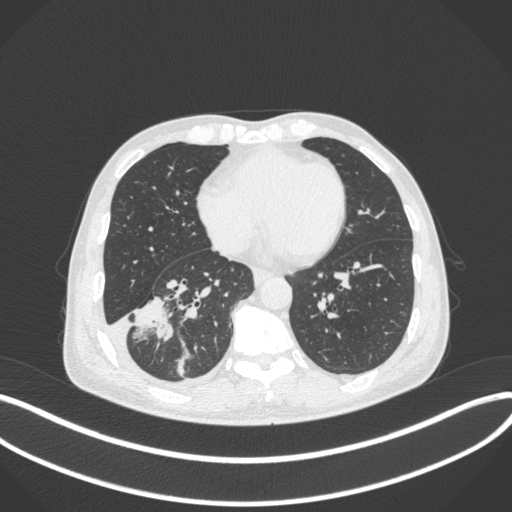
Chest CT, one axial slice; position 140 of 385 along the scan axis; 120 kVp; lung window (W 1500 / L -600 HU); 512 × 512 image matrix, field of view 400 × 400 mm. Patient: male, 64 years. Case-level facts recorded for this patient, not image findings: clinical TNM (as recorded): T3 N0 M0; histopathological grade: G2-3.
Structures marked on this image (rectangle marked by the reading radiologist):
- lung tumour (recorded histology: adenocarcinoma): bounding box <126,291,176,352> (left, top, right, bottom; pixels)